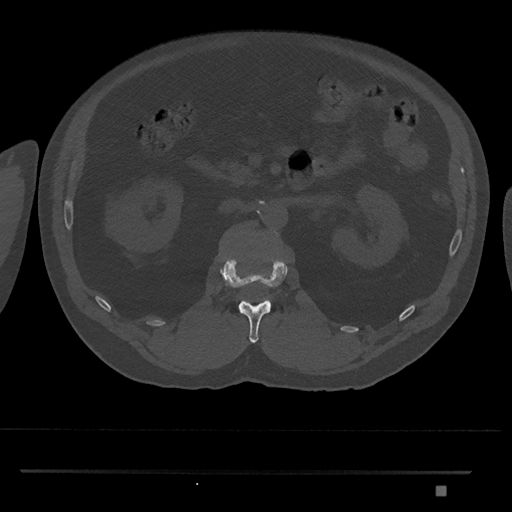
CT including the spine, one axial slice. Slice 801 of 1134 in the series (ordered by position). Reconstruction kernel Br40s/3. 120 kVp. Bone window (W 1800 / L 400 HU). 0.5 mm slice thickness. 512 × 512 image matrix, field of view 429 × 429 mm. Male patient, age 65 years. From the clinical record (not read from this slice): primary cancer: prostate.
Annotated regions visible in this slice (semi-automatic segmentation, software-assisted and operator-edited):
- L1 vertebra: bounding box <220,258,288,343> (left, top, right, bottom; pixels)
- L2 vertebra: <241,230,280,237>